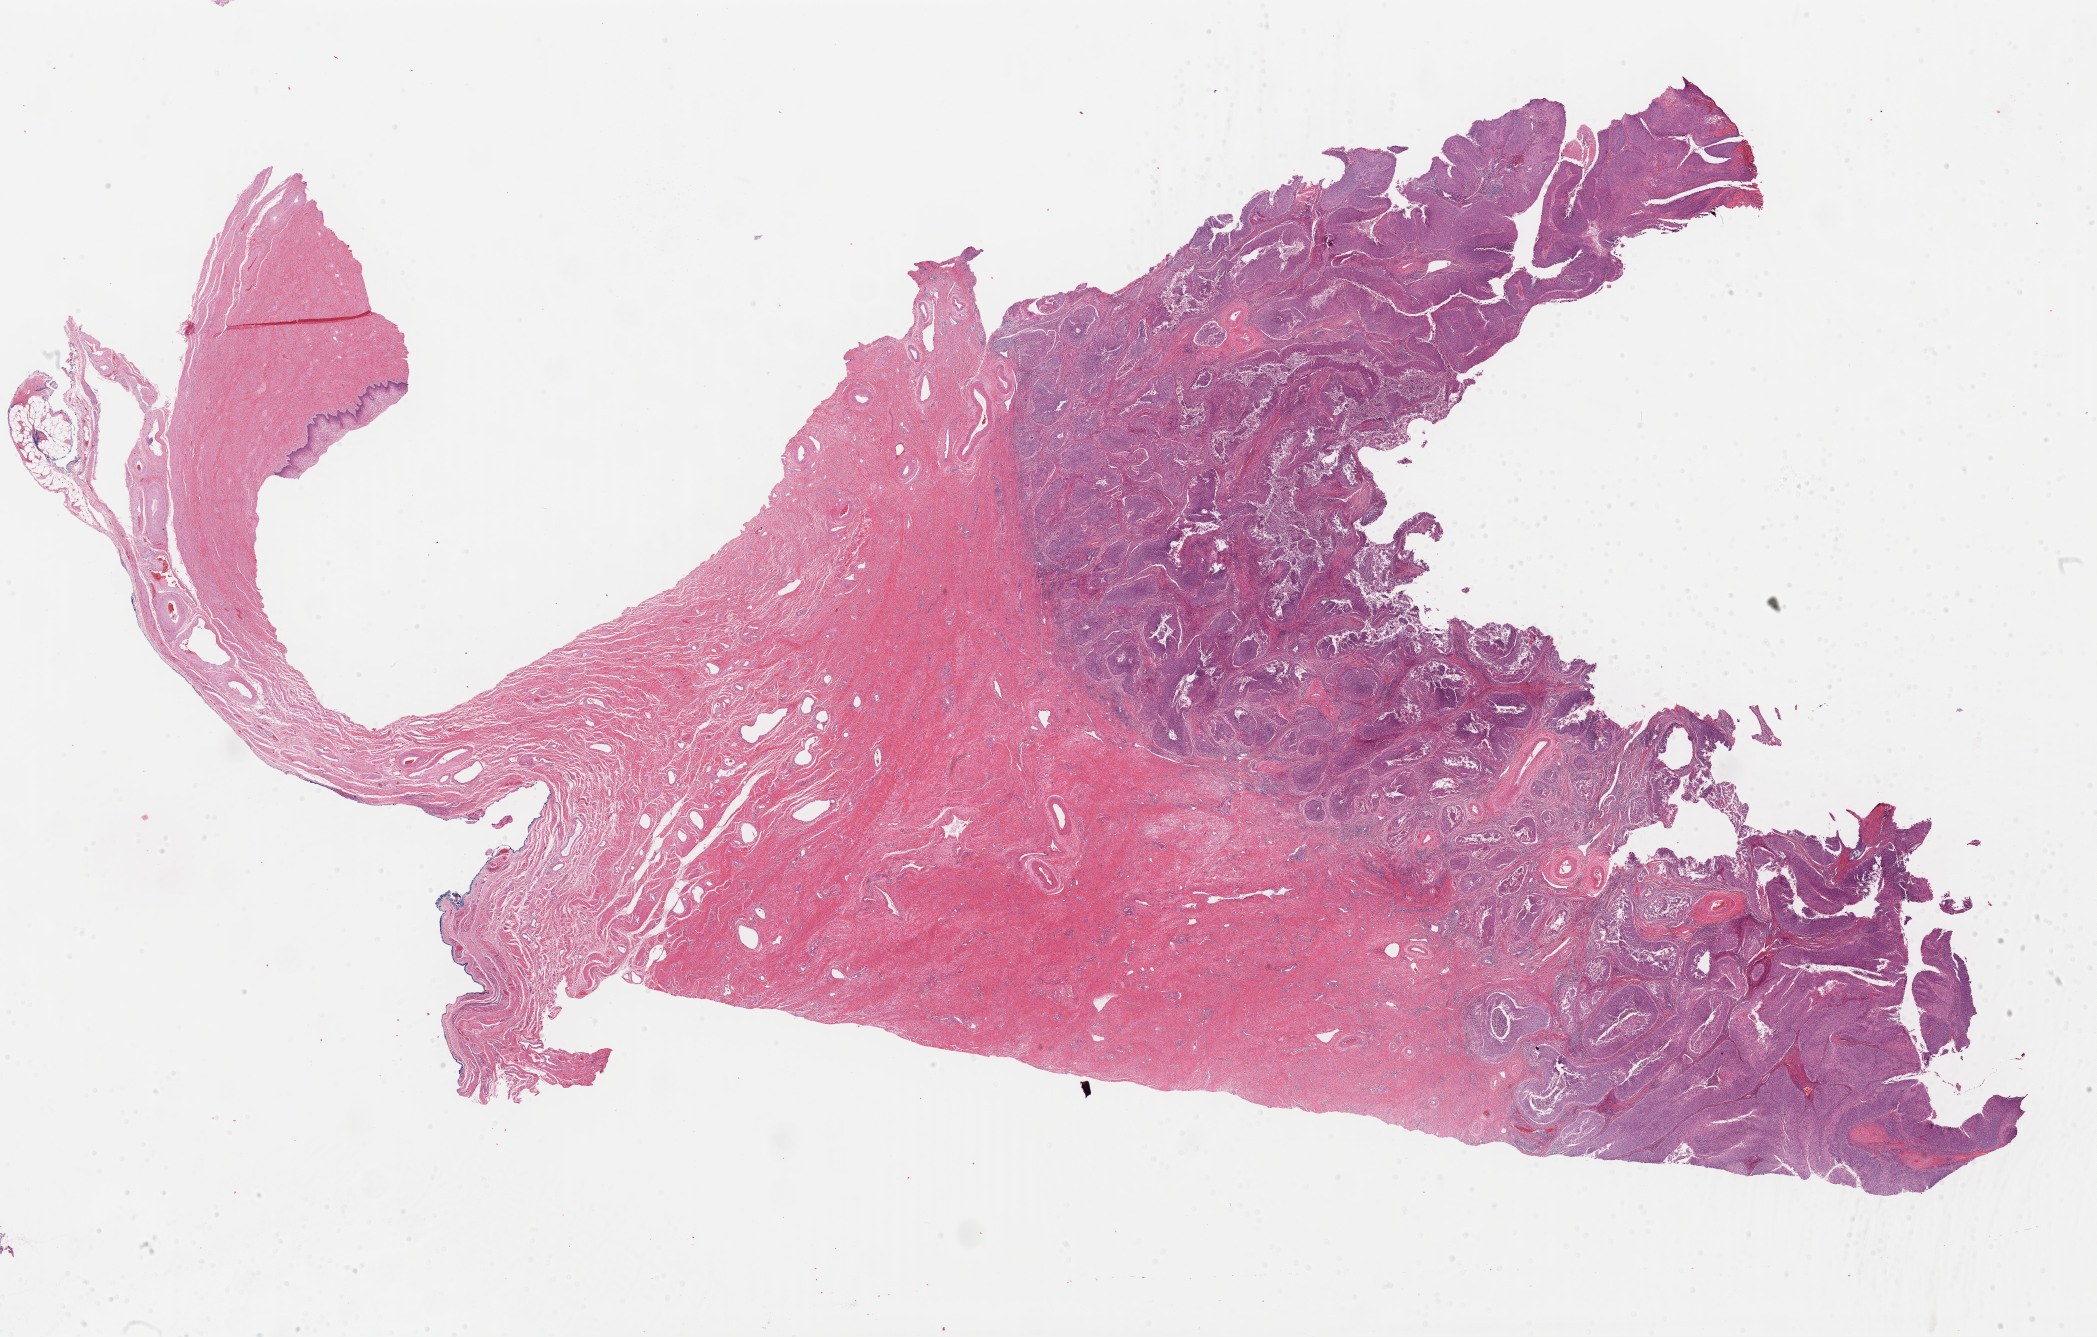
Whole-slide histology image, H&E — low-resolution overview of the scanned area, about 33.1 x 21.1 mm; formalin-fixed paraffin-embedded (FFPE) diagnostic section; primary tumour sample from the cervix. Patient: female, age at initial diagnosis 38 years. Histologic grade: G2 (moderately differentiated).
FIGO stage: IB2. Histologic diagnosis: Squamous cell carcinoma, NOS (cervix uteri).